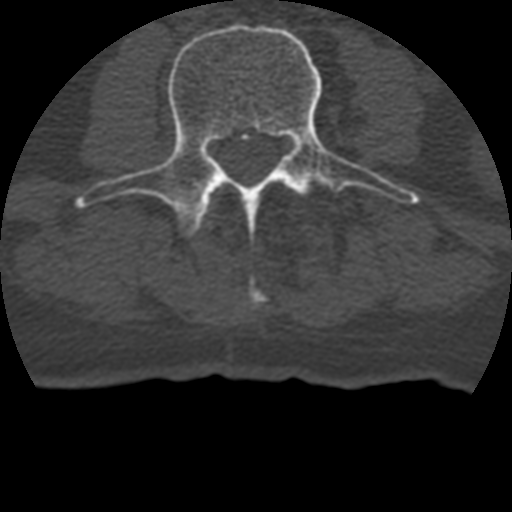
CT including the spine, one axial slice. Position 93 of 399 along the scan axis. 120 kVp. Bone window (W 1800 / L 400 HU). 1.25 mm slice thickness. 512 × 512 image matrix. Patient age 69 years. Case-level facts recorded for this patient, not image findings: primary cancer: prostate.
Annotated regions visible in this slice (semi-automatic segmentation, software-assisted and operator-edited):
- L2 vertebra: box from (x=249, y=288) to (x=264, y=307) px
- L3 vertebra: (x=77, y=23)–(x=413, y=235)